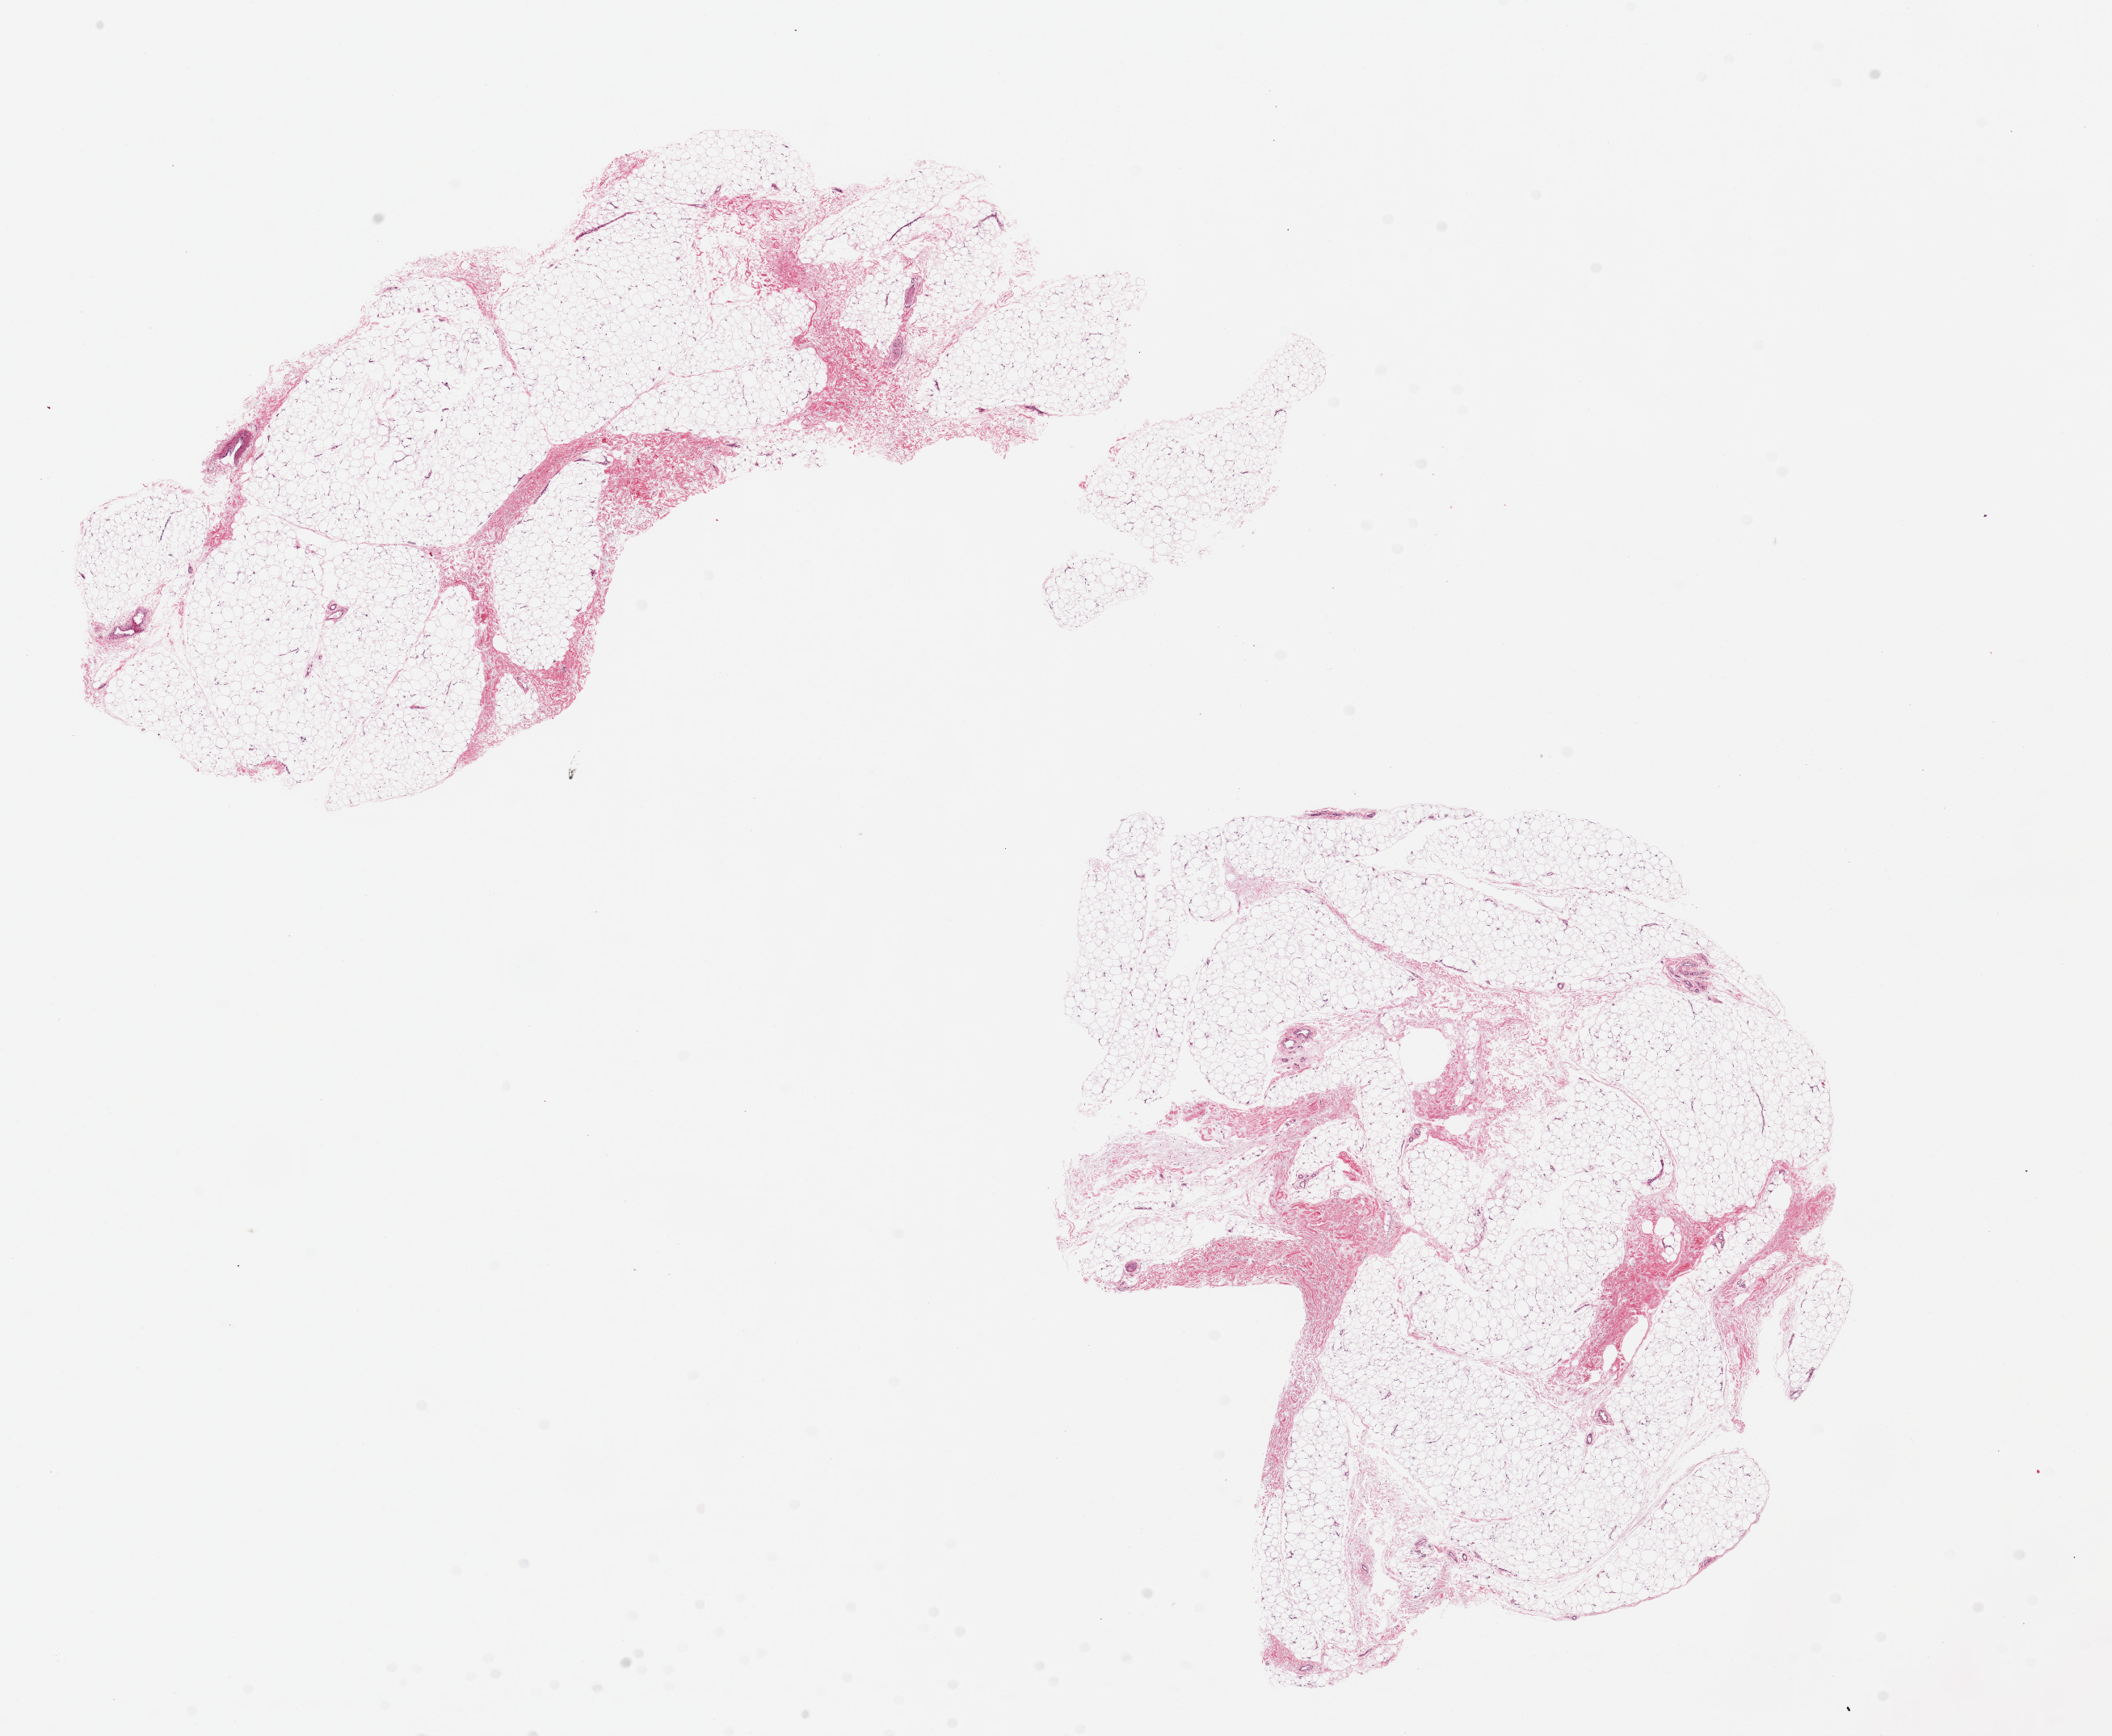
Digitized hematoxylin and eosin (H&E)-stained section, low-resolution overview of the scanned area, about 20.7 x 17.0 mm (slide scanned at 20x), PAXgene-fixed, paraffin-embedded tissue, target tissue: adipose tissue, donor tissue sample. Male donor.
Review note (as recorded): 1 pieces ~8x7mm.